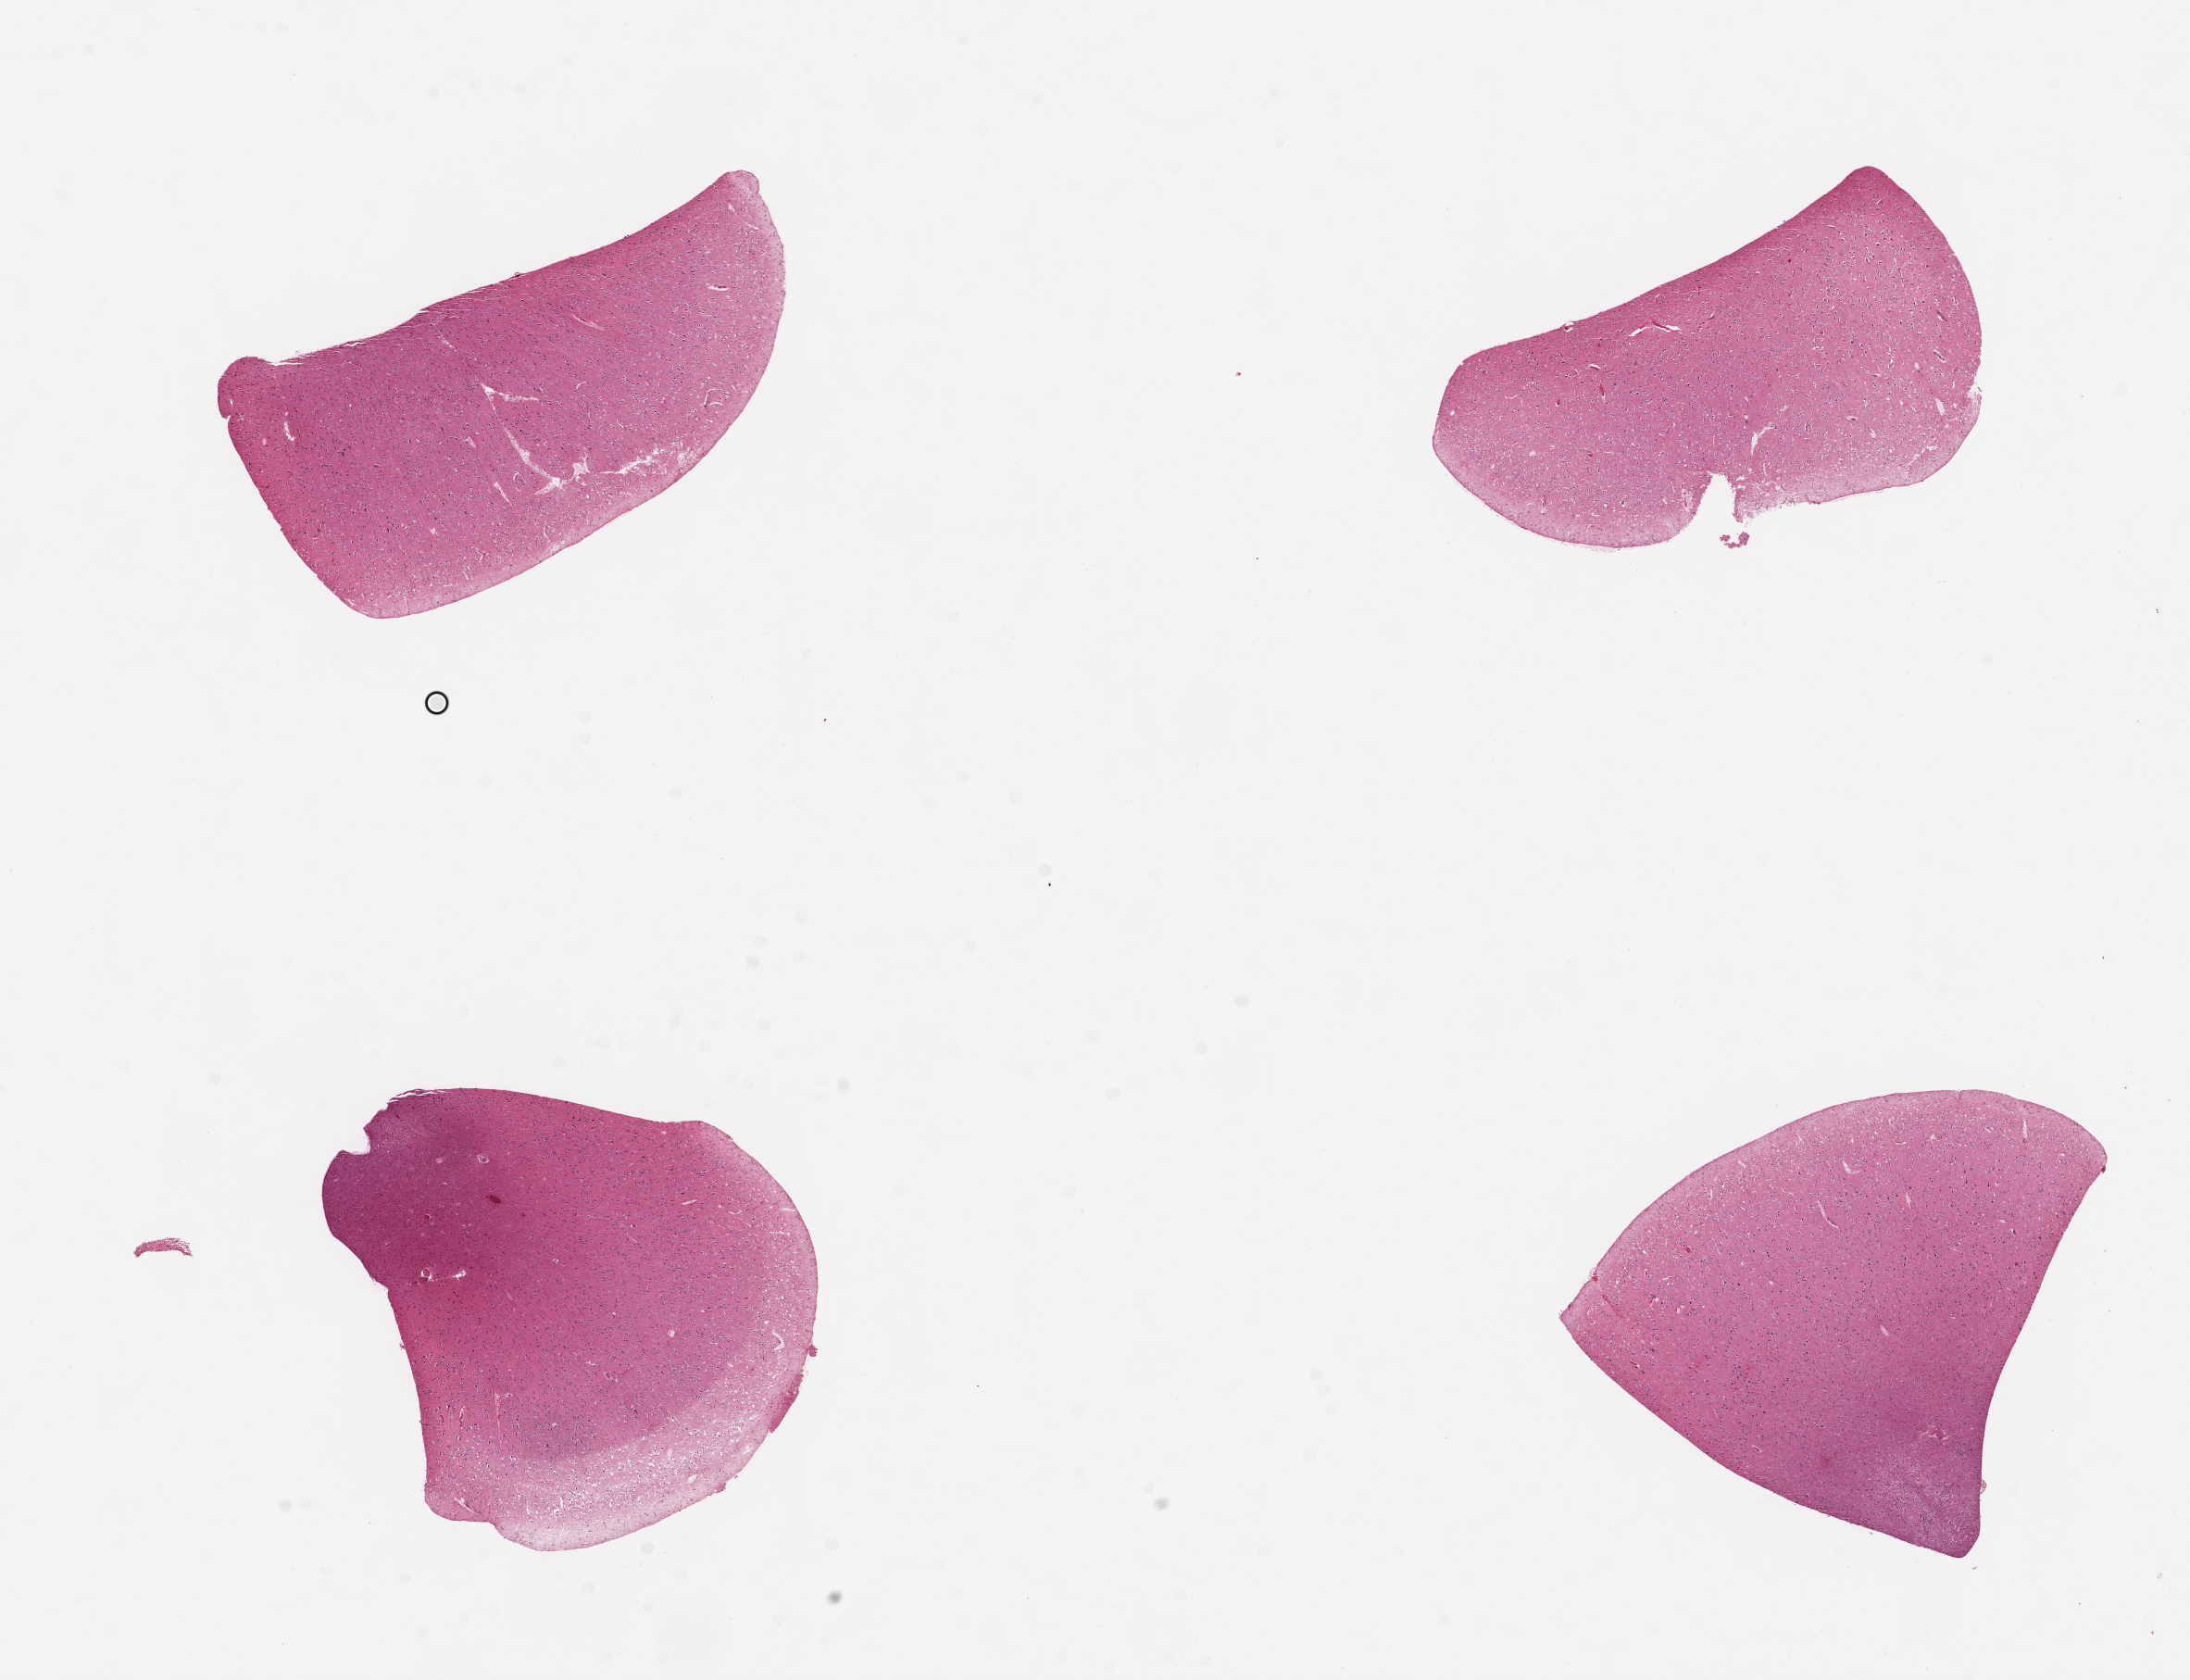
H&E whole-slide image, brightfield, shown as a low-resolution overview of the whole scanned area (about 18.7 x 14.3 mm); PAXgene-fixed paraffin-embedded (PFPE) section; sampled site (target tissue): cerebral cortex; tissue donor sample. Male donor.
Pathologist's review note for this sample: 4 pieces, up to 5x2.5mm.